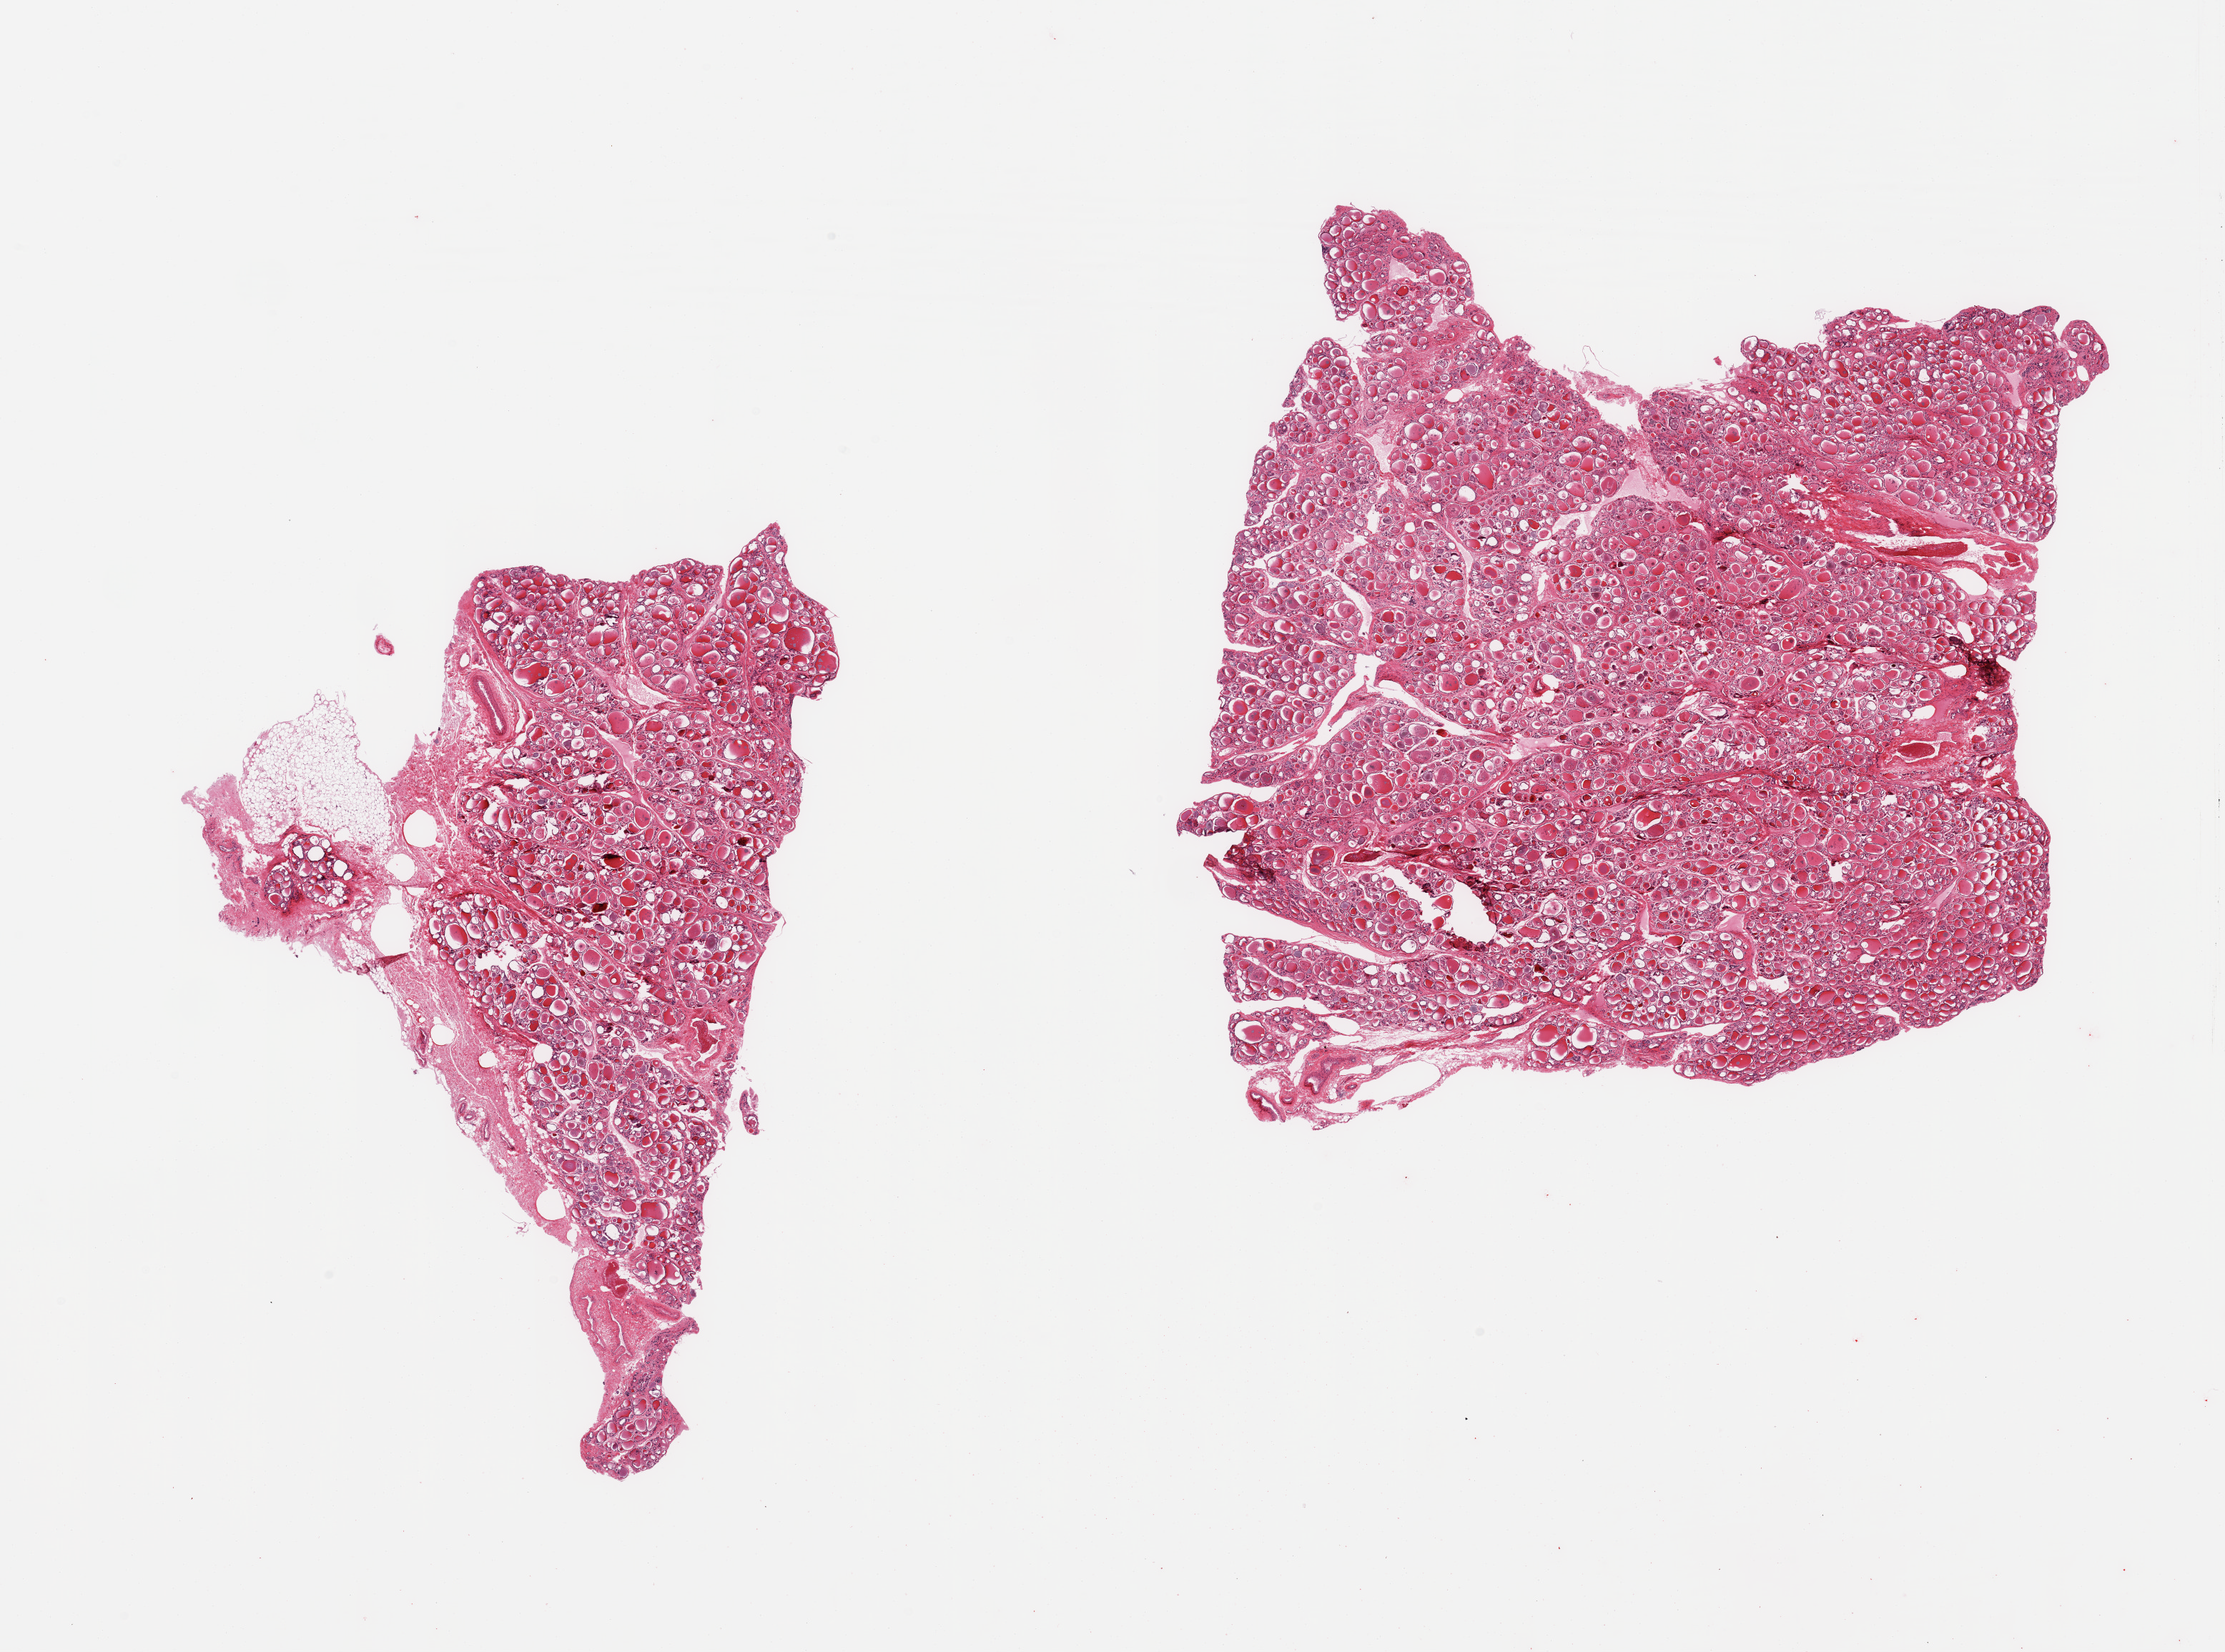
Haematoxylin and eosin whole-slide image — low-resolution overview of the scanned area, about 24.6 x 18.3 mm; PAXgene-fixed, paraffin-embedded tissue; sampled site (target tissue): thyroid; donor tissue sample. Donor sex: female.
Pathologist's review note for this sample: 2 pieces, no abnormalities.